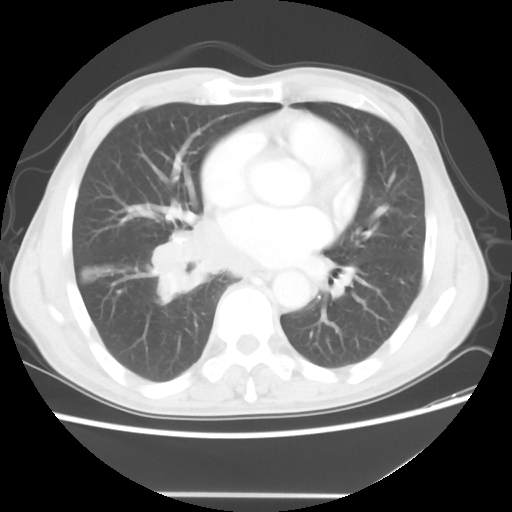
Chest CT, one axial slice; position 25 of 56 along the scan axis; reconstruction kernel STANDARD; 120 kVp; lung window (W 1500 / L -600 HU); 512 × 512 image matrix, field of view 344 × 344 mm. Patient: male, 65 years. Case-level facts recorded for this patient, not image findings: clinical TNM (as recorded): T1c N3 M0; histopathological grade: G3.
Annotated regions visible in this slice (bounding box drawn by a radiologist):
- lung tumour (recorded histology: small cell carcinoma): bounding box (x1, y1, x2, y2) in pixels: (149, 208, 275, 303)